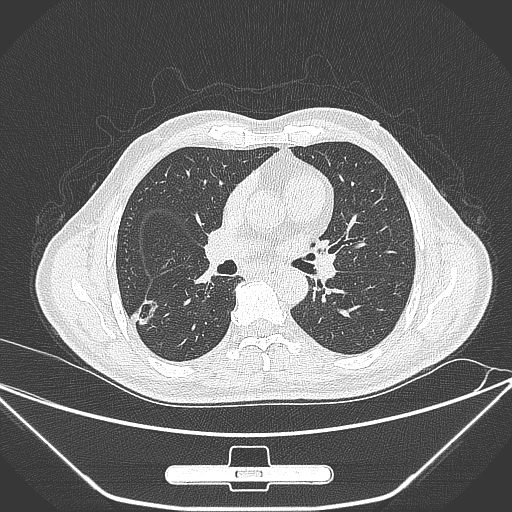
Chest CT, one axial slice. Lung window (W 1500 / L -600 HU). 1 mm slice thickness. 512 × 512 image matrix, field of view 398 × 398 mm. Patient: male, 71 years. Case-level facts recorded for this patient, not image findings: clinical TNM (as recorded): T1c N0 M0; histopathological grade: G2.
Annotated regions visible in this slice (bounding box drawn by a radiologist):
- lung tumour (recorded histology: adenocarcinoma): bounding box [x1, y1, x2, y2] px = [135, 295, 164, 327]